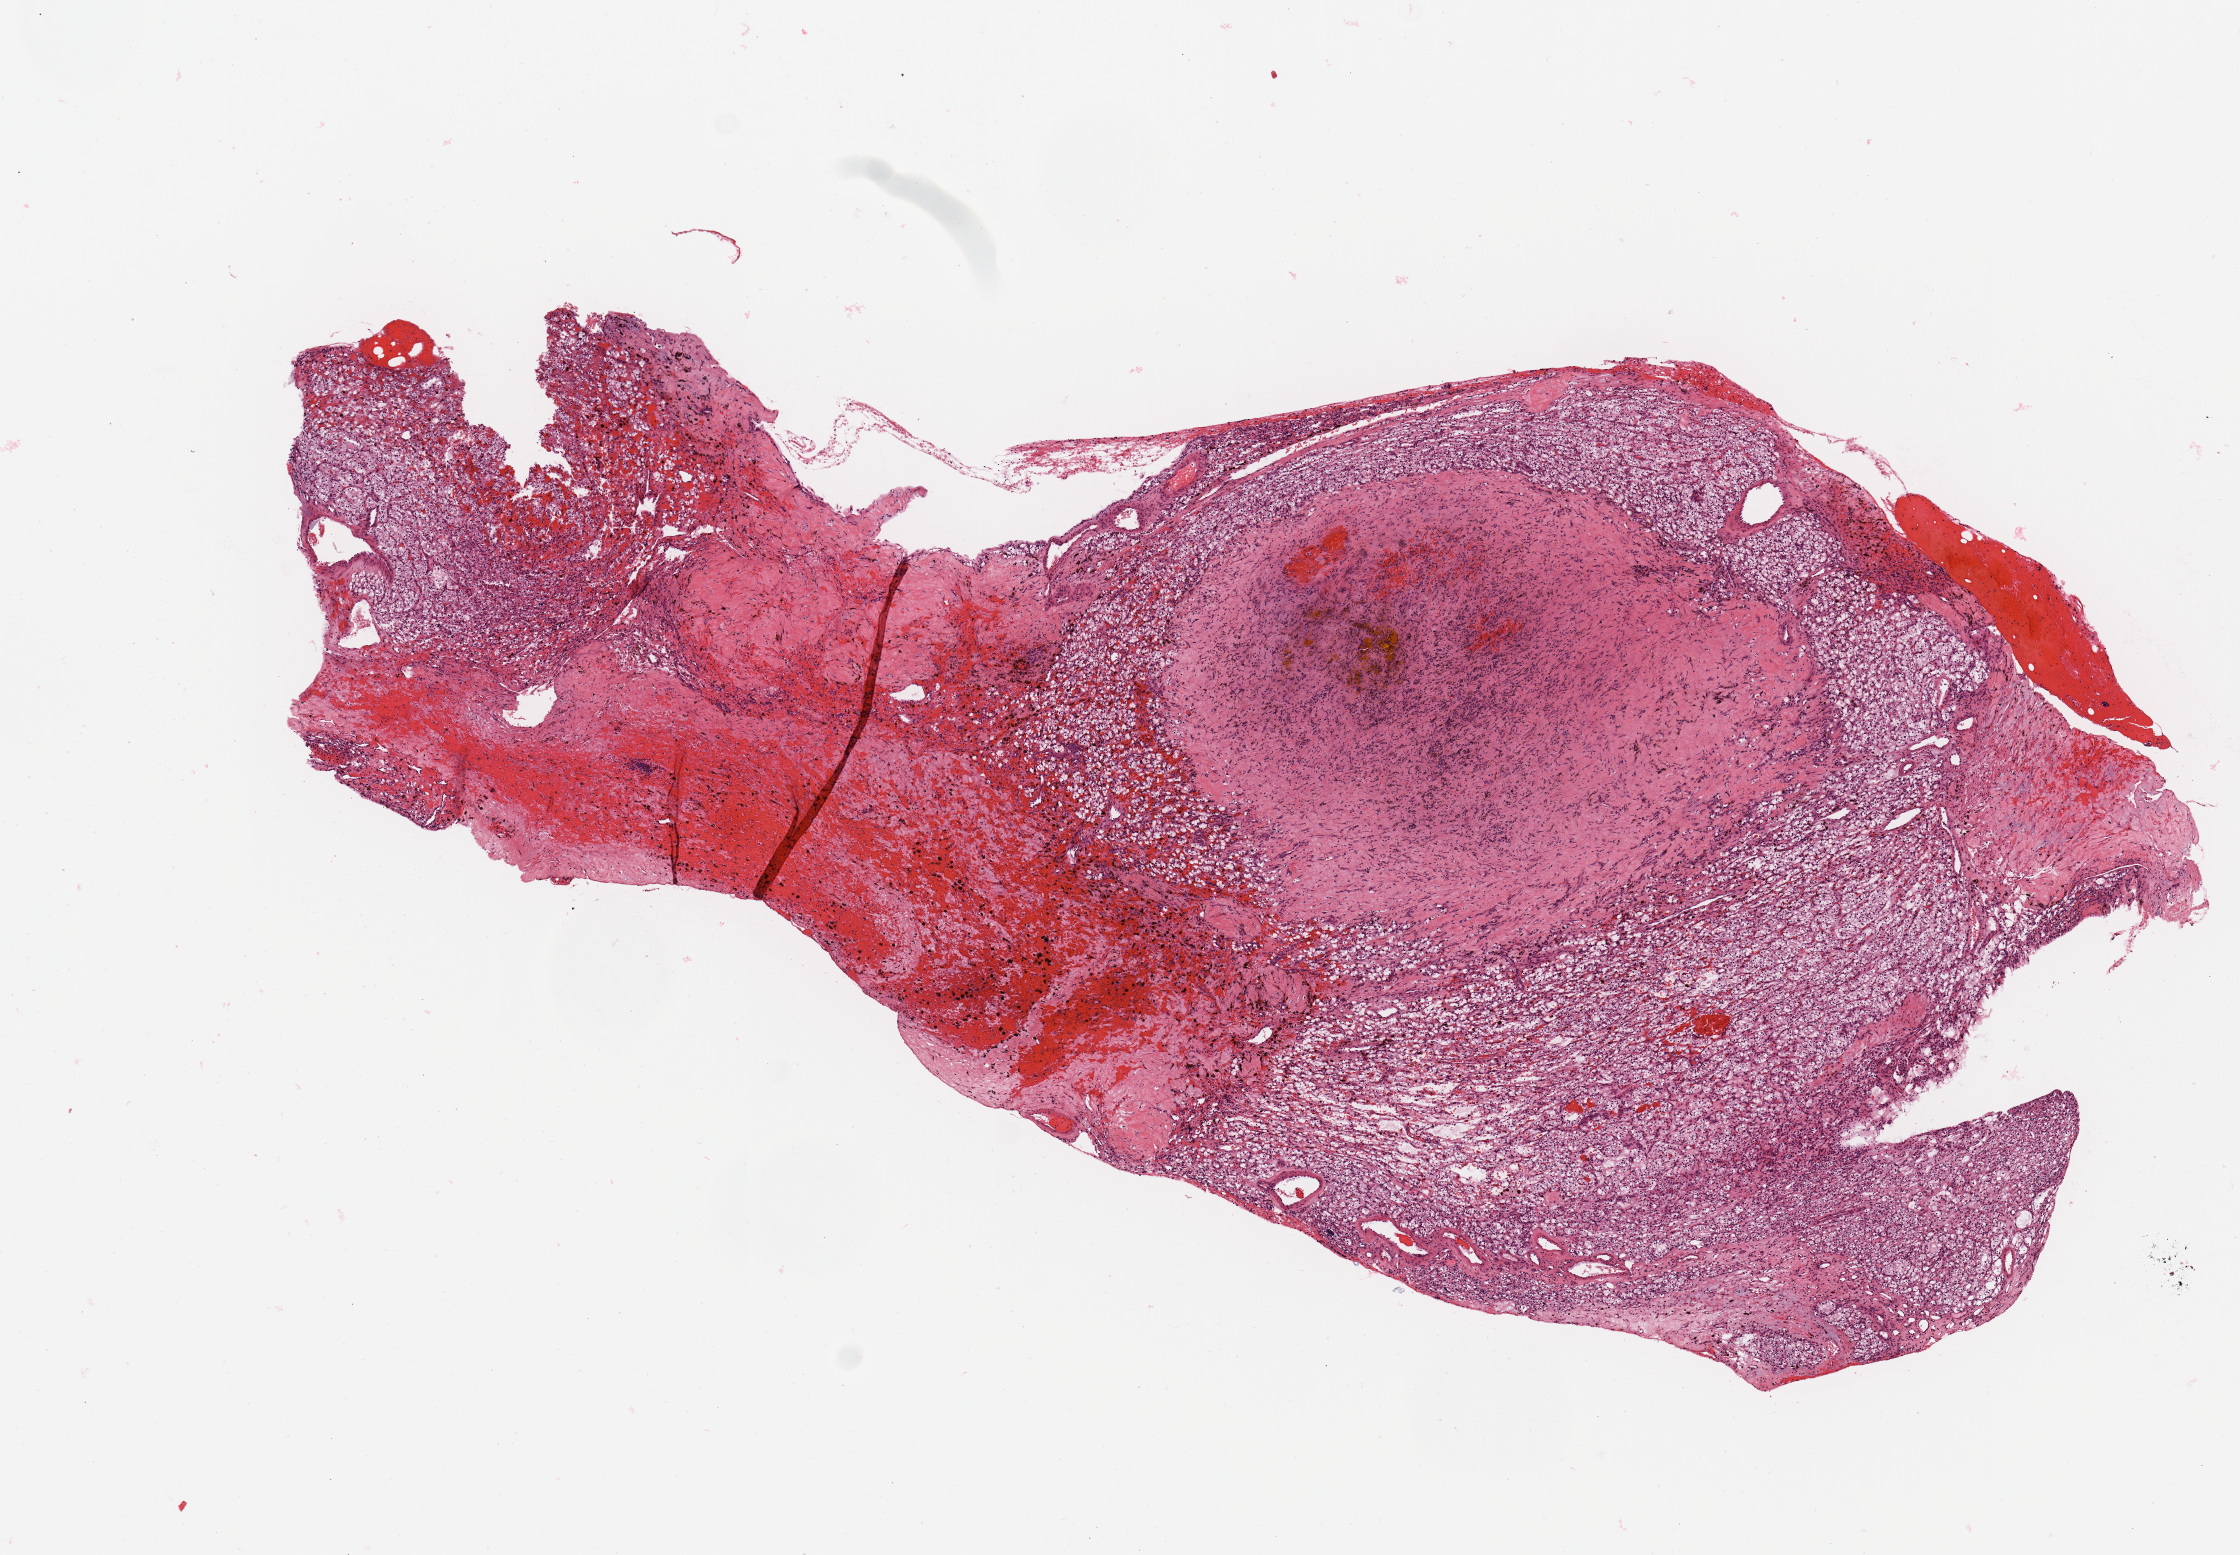
H&E-stained whole-slide image, shown as a low-resolution overview of the whole scanned area (about 8.9 x 6.2 mm), tumour tissue sample, kidney. Female, 64 y/o. Histologic grade: G2 (moderately differentiated).
Primary tumour site (as recorded): lower pole. Diagnosis: Renal cell carcinoma, NOS. AJCC pathologic stage: I.